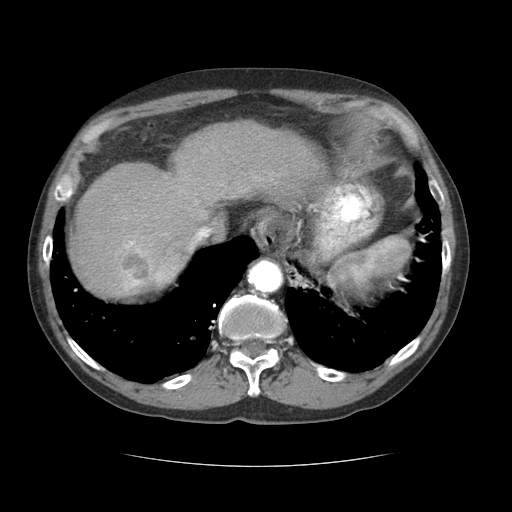
Contrast-enhanced abdominal CT (liver protocol), one axial slice; slice 54 of 69 in the series (ordered by position); reconstruction kernel STANDARD; soft-tissue window (W 400 / L 40 HU); 2.5 mm slice thickness; 512 × 512 image matrix, field of view 360 × 360 mm. Case-level facts recorded for this patient, not image findings: diagnosis: hepatocellular carcinoma (patient treated with transarterial chemoembolisation; whether this scan precedes or follows treatment is not stated here); TNM stage (as recorded): Stage-II; Child-Pugh class: B; tumour differentiation: poorly differentiated; tumour nodularity: multinodular.
Outlined on this slice (semi-automatically segmented with operator editing):
- abdominal aorta: bounding box (x1, y1, x2, y2) in pixels: (248, 260, 281, 292)
- liver parenchyma outside the tumour (the mass and vessels are separate outlines, so this box may not span the whole liver): (68, 120, 328, 296)
- mass: (106, 239, 183, 295)